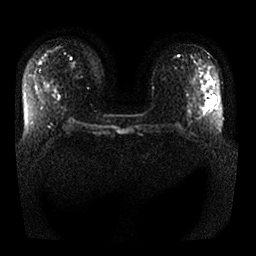
Breast MRI, one axial slice; position 16 of 25 along the scan axis; diffusion-weighted series; image 2 of 4 stored at this slice position (different b-values; order by instance number); 1.5 T; 4 mm slice thickness; 256 × 256 image matrix, field of view 360 × 360 mm. Female patient.
Annotated regions visible in this slice (outlined manually by an expert reader):
- tumour on diffusion-weighted imaging: bounding box <207,96,216,108> (left, top, right, bottom; pixels)